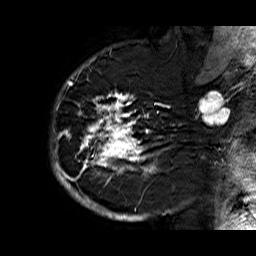
Breast MRI (dynamic contrast-enhanced), one sagittal slice. Position 46 of 60 along the scan axis. Dynamic contrast-enhanced series, time point 2 of 6 at this slice position (early post-contrast). 1.5 T. TE 6.3 ms, TR 32.9 ms. 4 mm slice thickness. 256 × 256 image matrix, field of view 200 × 200 mm. Female patient. From the clinical record (not read from this slice): setting: breast cancer imaged before/during neoadjuvant chemotherapy; receptor status: HR-positive, HER2-negative.
Outlined on this slice (semi-automatically segmented with operator editing):
- analysis volume of interest (the breast-tissue region the enhancement analysis was run in; not a lesion): bounding box <51,74,176,210> (left, top, right, bottom; pixels)
- tumour enhancement mask (voxels above the 100 % enhancement threshold inside the analysis volume of interest): <52,74,163,210>